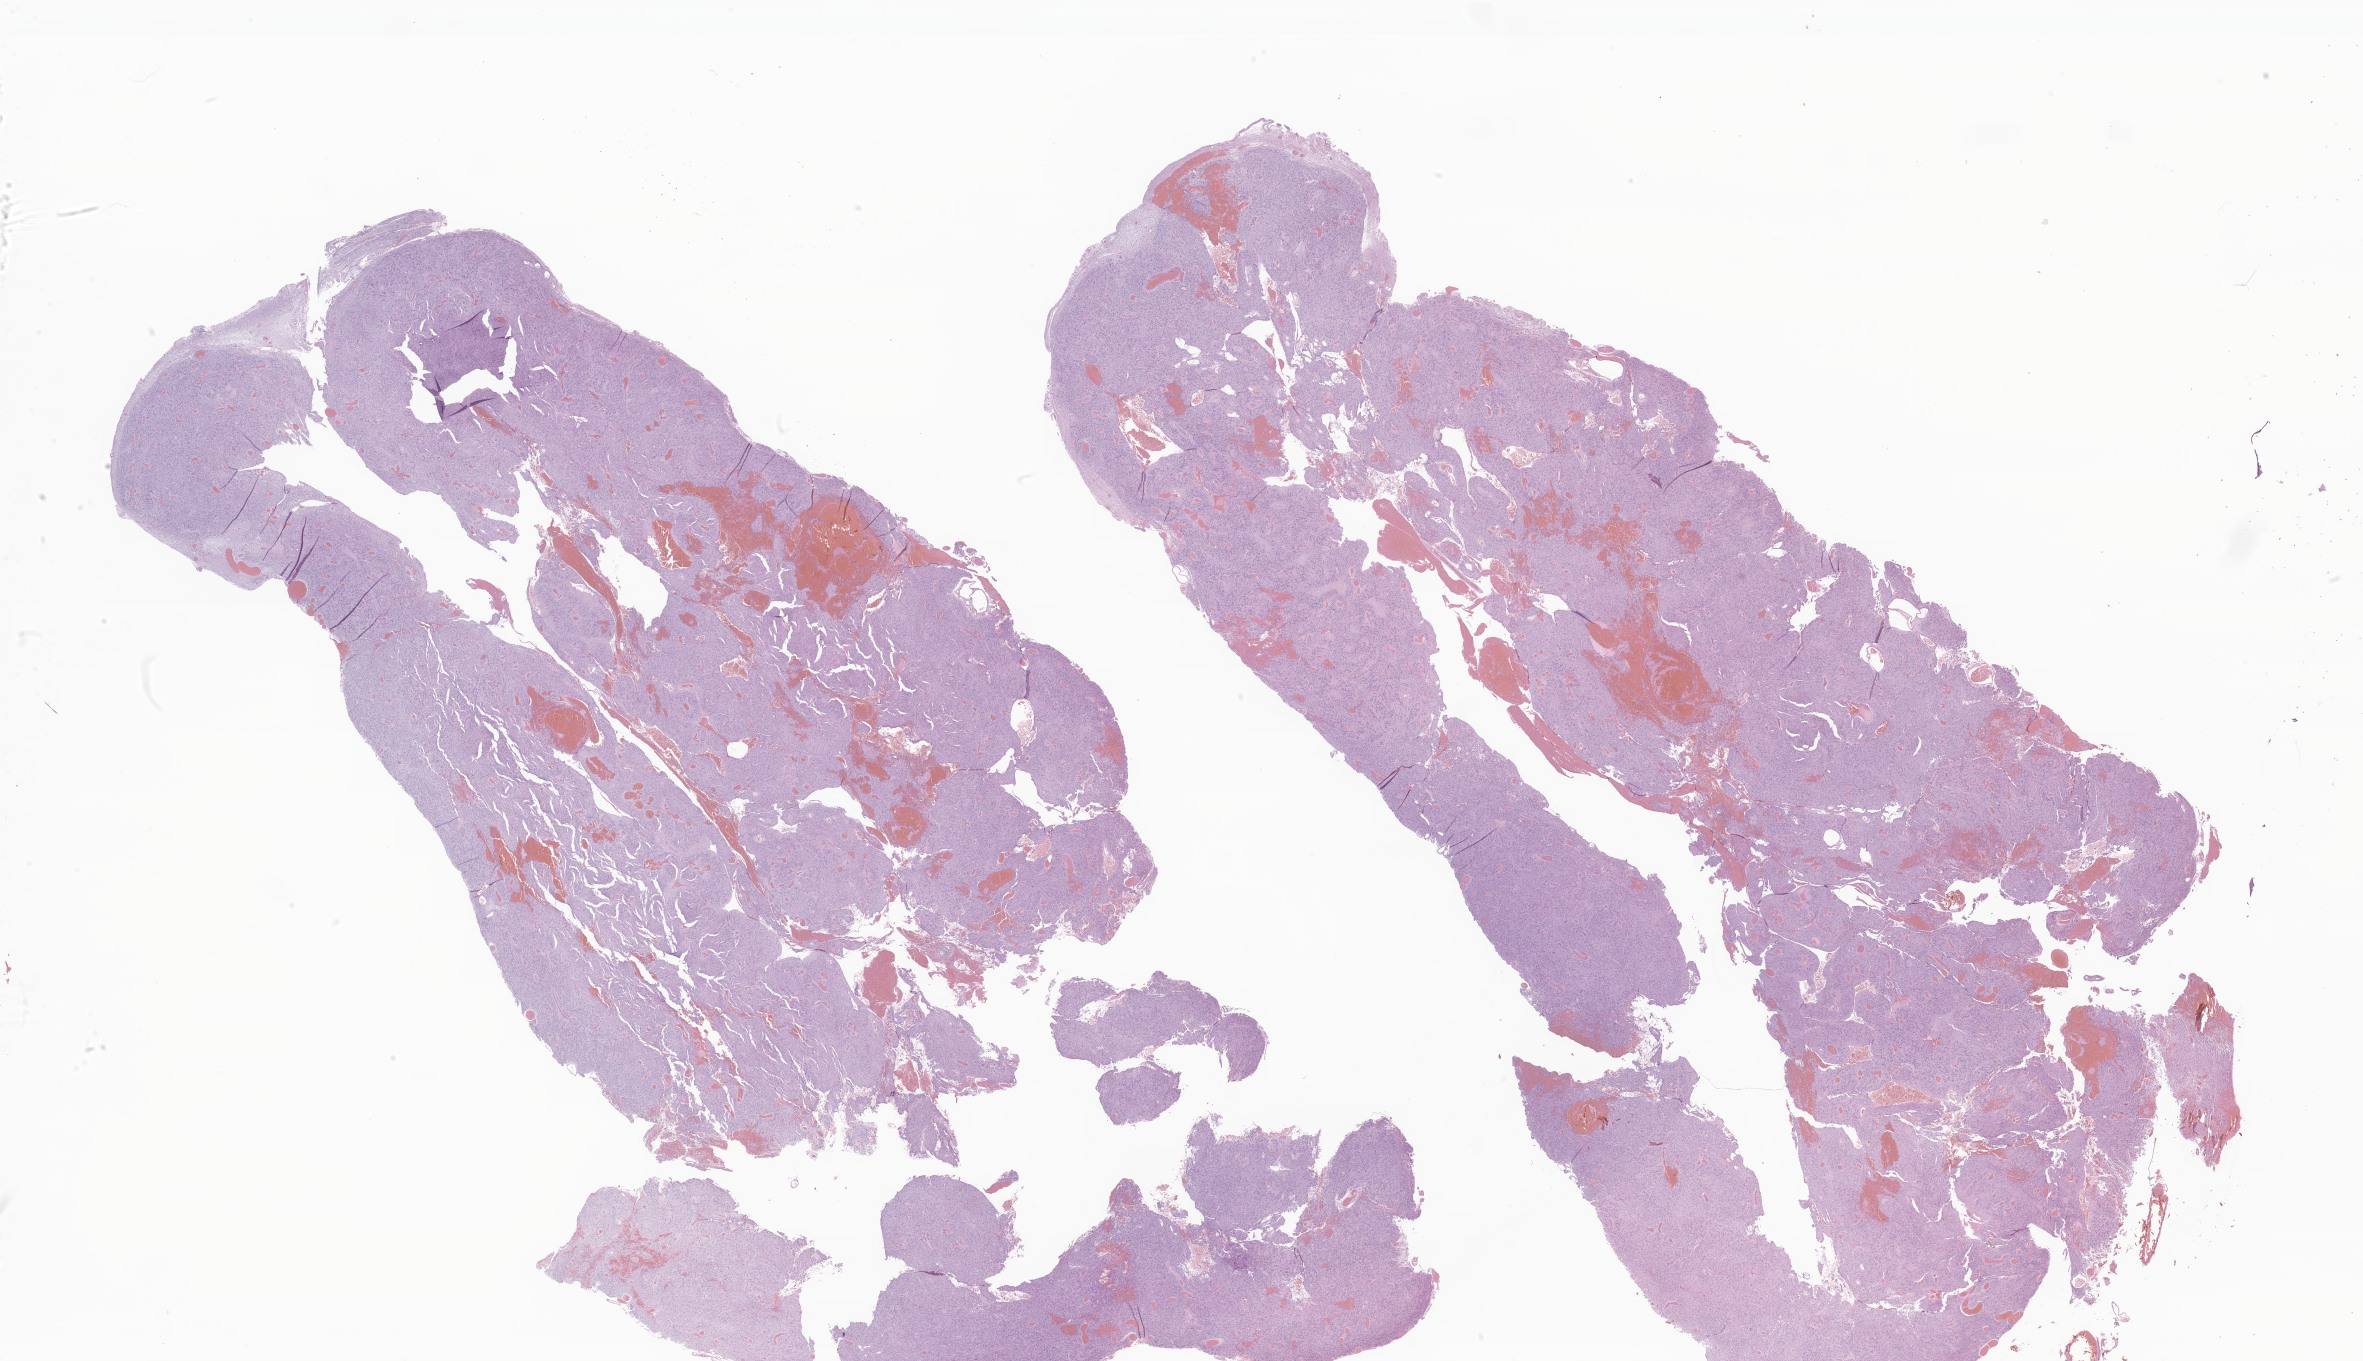
Hematoxylin and eosin (H&E) whole-slide image of tumor tissue from the spinal cord, a low-resolution overview of the entire scanned area, about 39.9 x 23.0 mm, formalin-fixed, paraffin-embedded (FFPE) tissue. Male patient, age 205 months (17 years 1 month).
Diagnosis: Ependymoma, NOS.